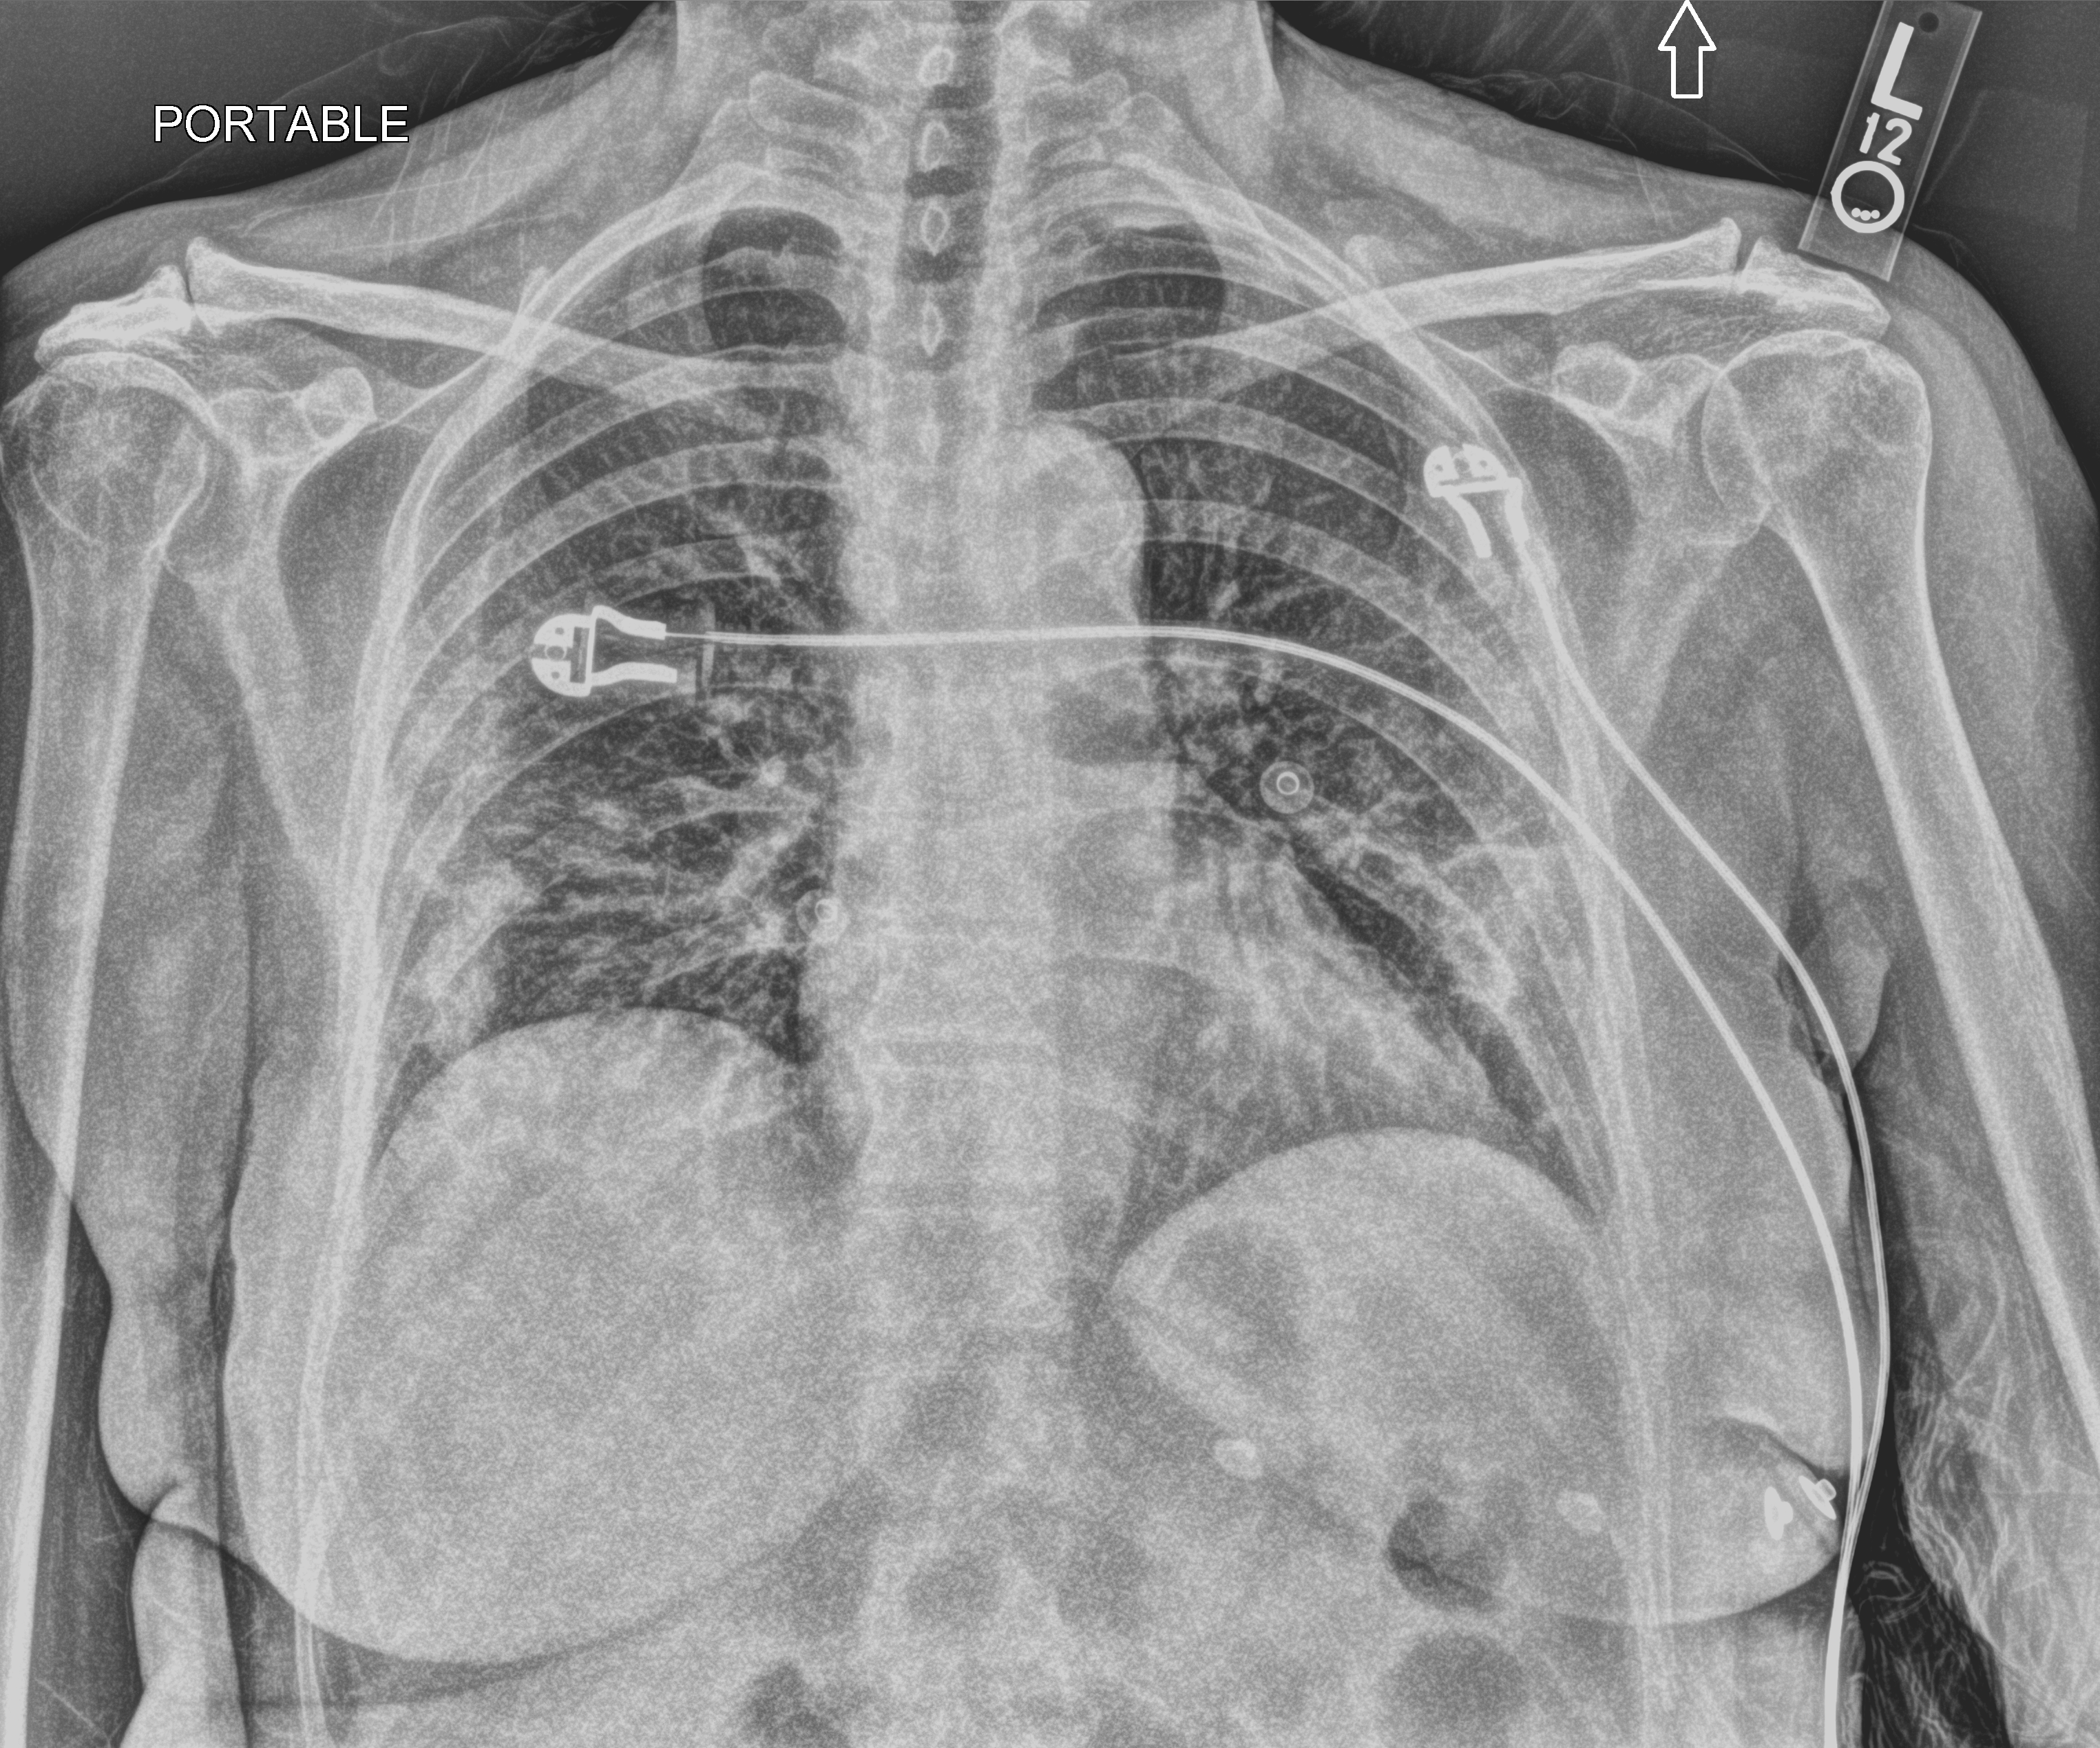
Bedside chest radiograph (computed radiography); anteroposterior (AP) projection. Patient hospitalised with COVID-19; female, aged 60–74 years.
Admission-level facts for this patient (not findings on this image; timing relative to this image not recorded): mechanically ventilated during this hospital stay: yes; length of hospital stay: 18 days; hypertension (admission record): yes.